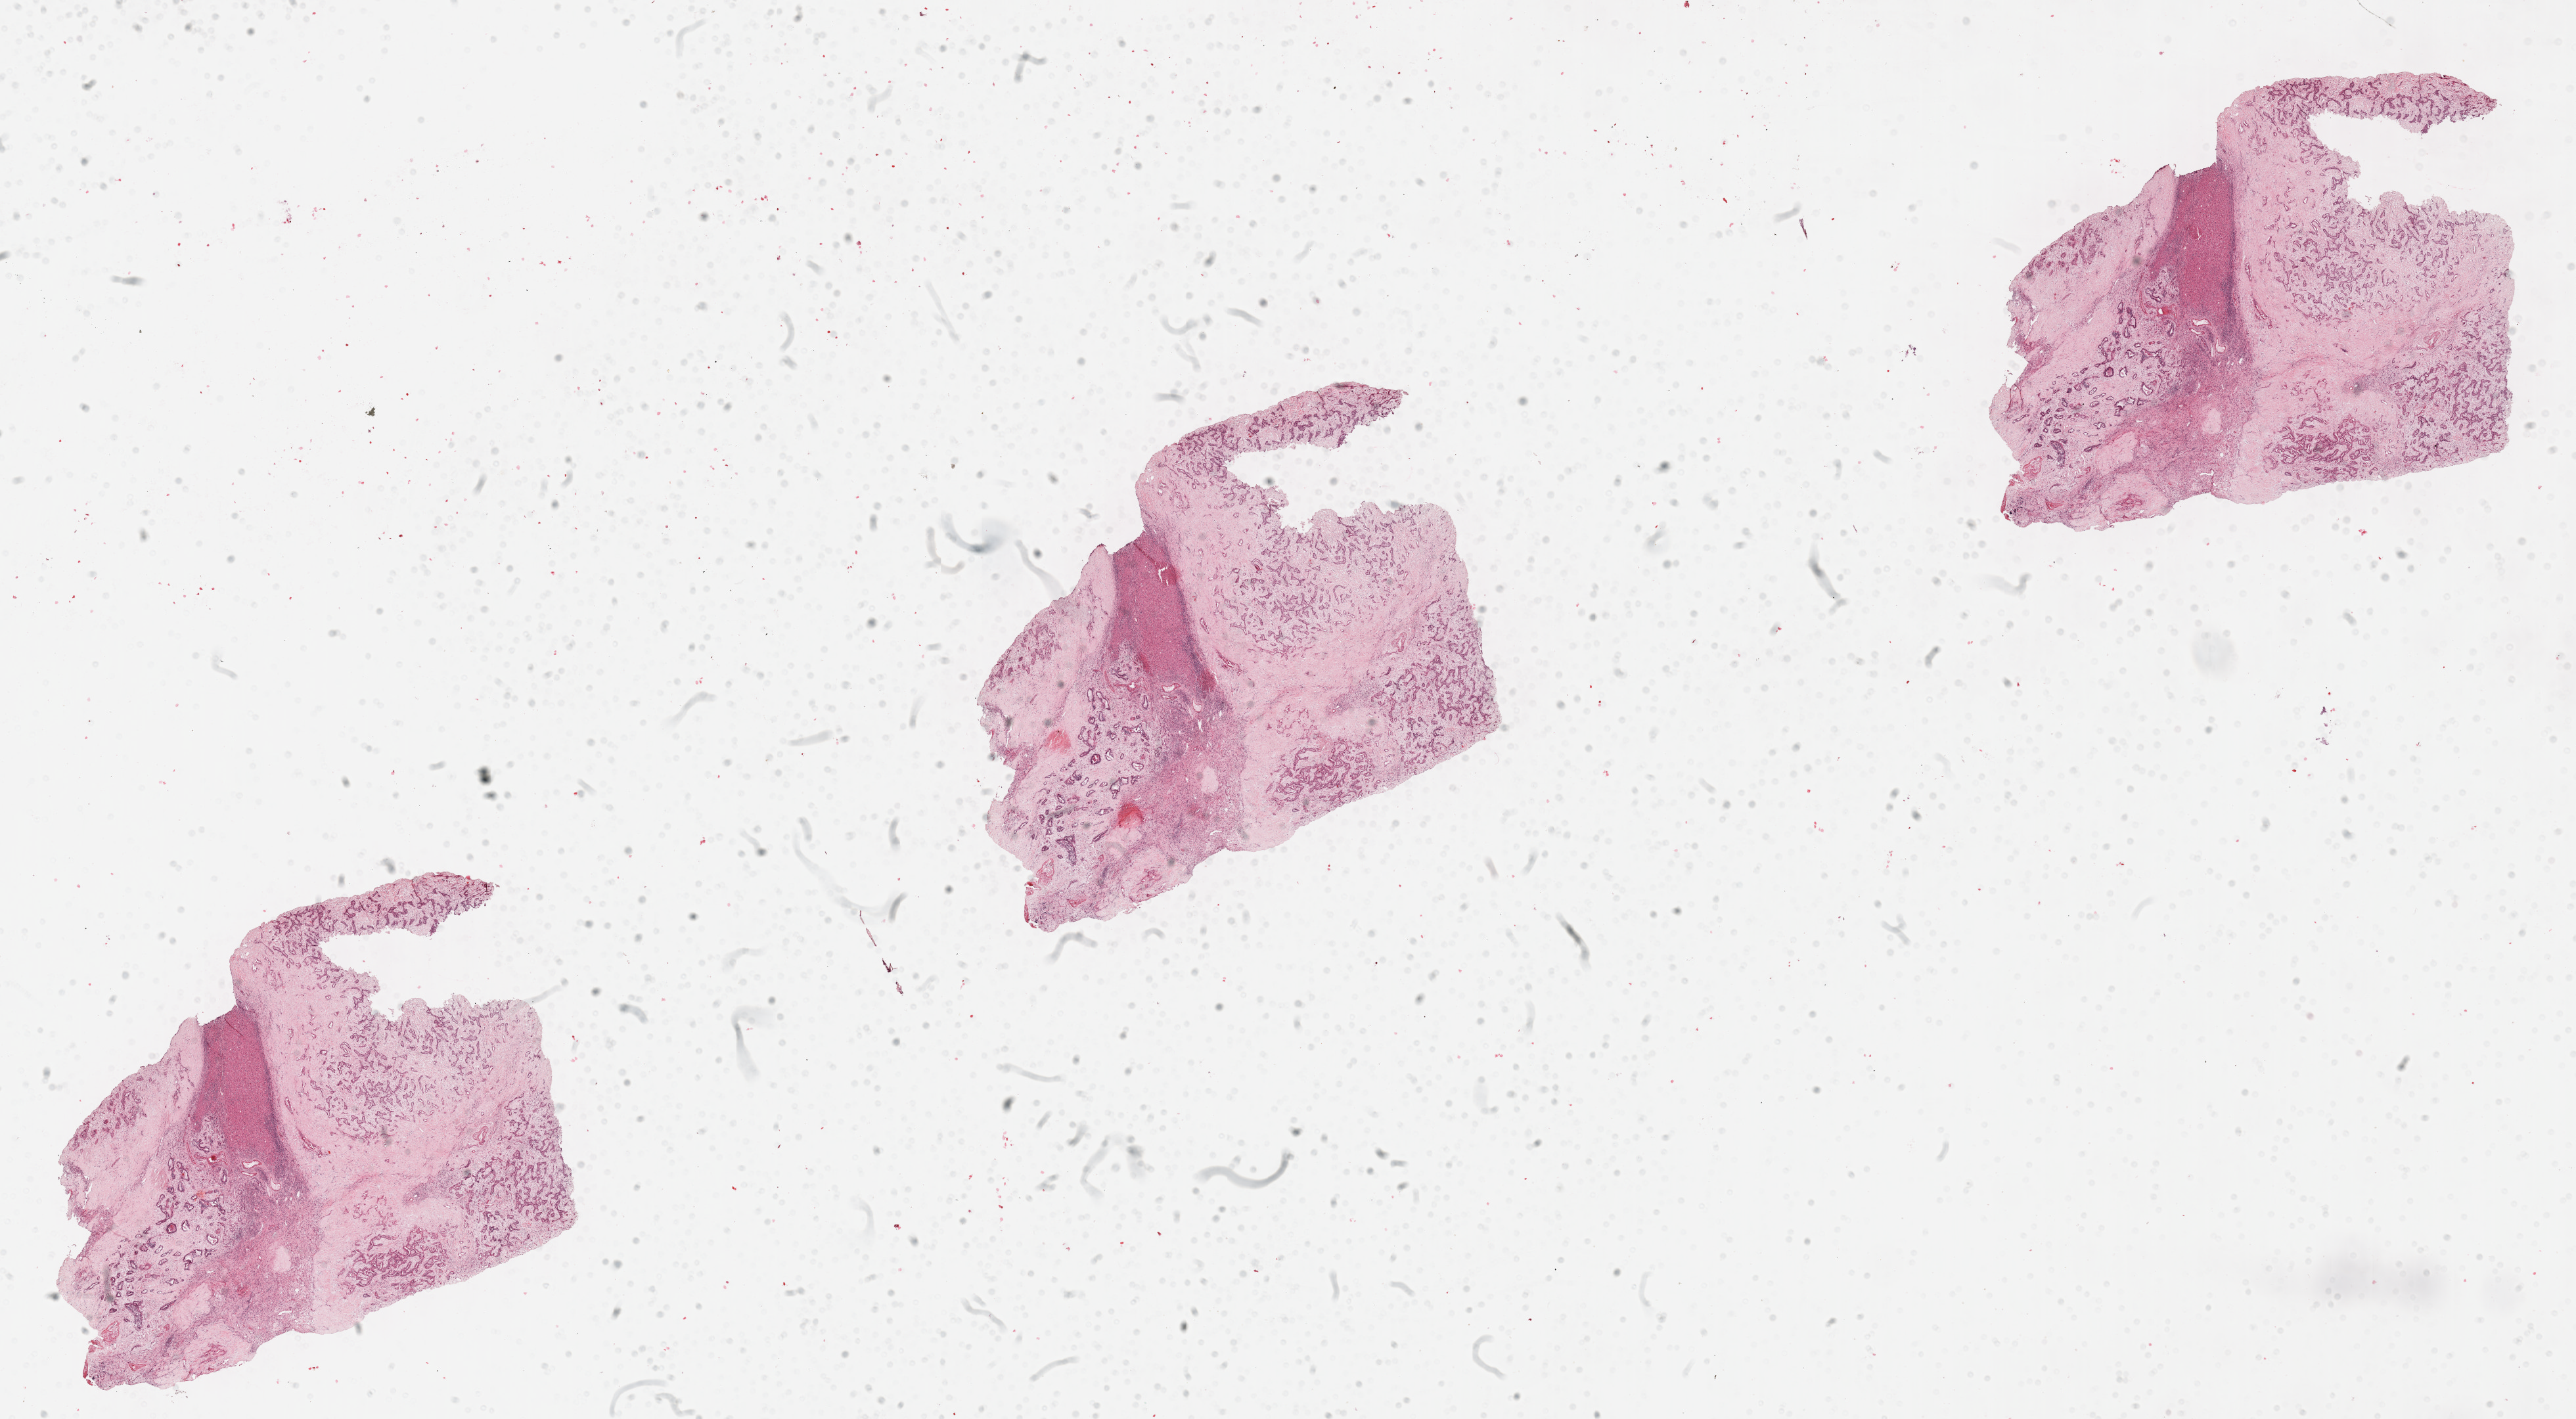
Whole-slide histology image, Hematoxylin and eosin (H&E) stained — whole scanned area (about 31.7 x 17.5 mm) shown as a low-resolution overview; formalin-fixed paraffin-embedded (FFPE) diagnostic section; sample: primary tumour, bile duct. Patient: male, age at initial diagnosis 62 years.
Pathologic diagnosis: Cholangiocarcinoma (intrahepatic bile duct).